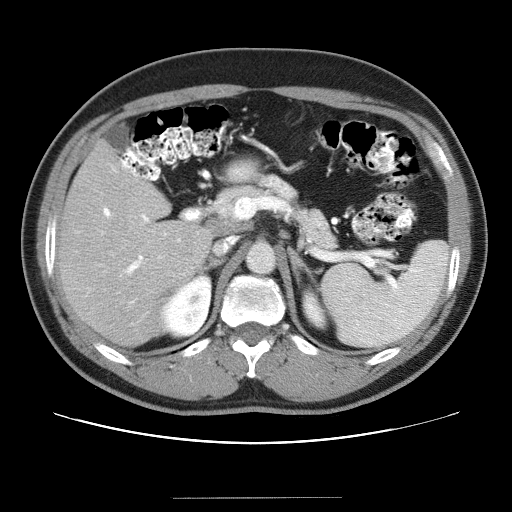
Contrast-enhanced abdominal CT (liver protocol), one axial slice; reconstruction kernel STANDARD; soft-tissue window (W 400 / L 40 HU); 5 mm slice thickness; 512 × 512 image matrix, field of view 380 × 380 mm. From the clinical record (not read from this slice): diagnosis: hepatocellular carcinoma (patient treated with transarterial chemoembolisation; whether this scan precedes or follows treatment is not stated here); TNM stage (as recorded): Stage-IVA; Child-Pugh class: B.
Structures marked on this image (semi-automatic segmentation, software-assisted and operator-edited):
- liver parenchyma outside the tumour (the mass and vessels are separate outlines, so this box may not span the whole liver): bounding box (x1, y1, x2, y2) in pixels: (56, 139, 216, 346)
- liver vessels: (78, 165, 198, 304)